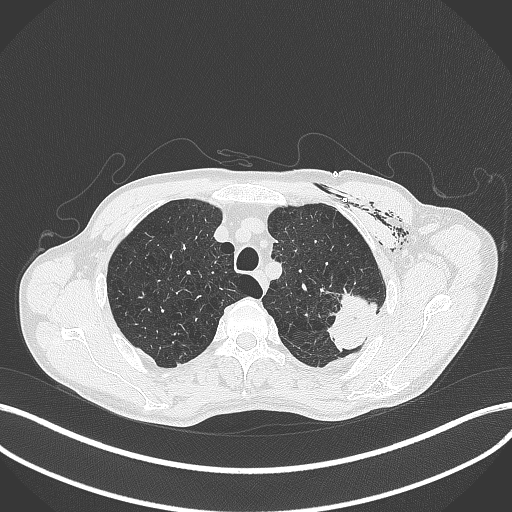
Chest CT, one axial slice. Slice 335 of 457 in the series (ordered by position). Reconstruction kernel B70f. 120 kVp. Lung window (W 1500 / L -600 HU). 512 × 512 image matrix, field of view 400 × 400 mm. Male patient, age 58 years. Case-level facts recorded for this patient, not image findings: clinical TNM (as recorded): T3 N0 M0.
Annotated regions visible in this slice (bounding box drawn by a radiologist):
- lung tumour (recorded histology: adenocarcinoma): bounding box <327,283,378,353> (left, top, right, bottom; pixels)